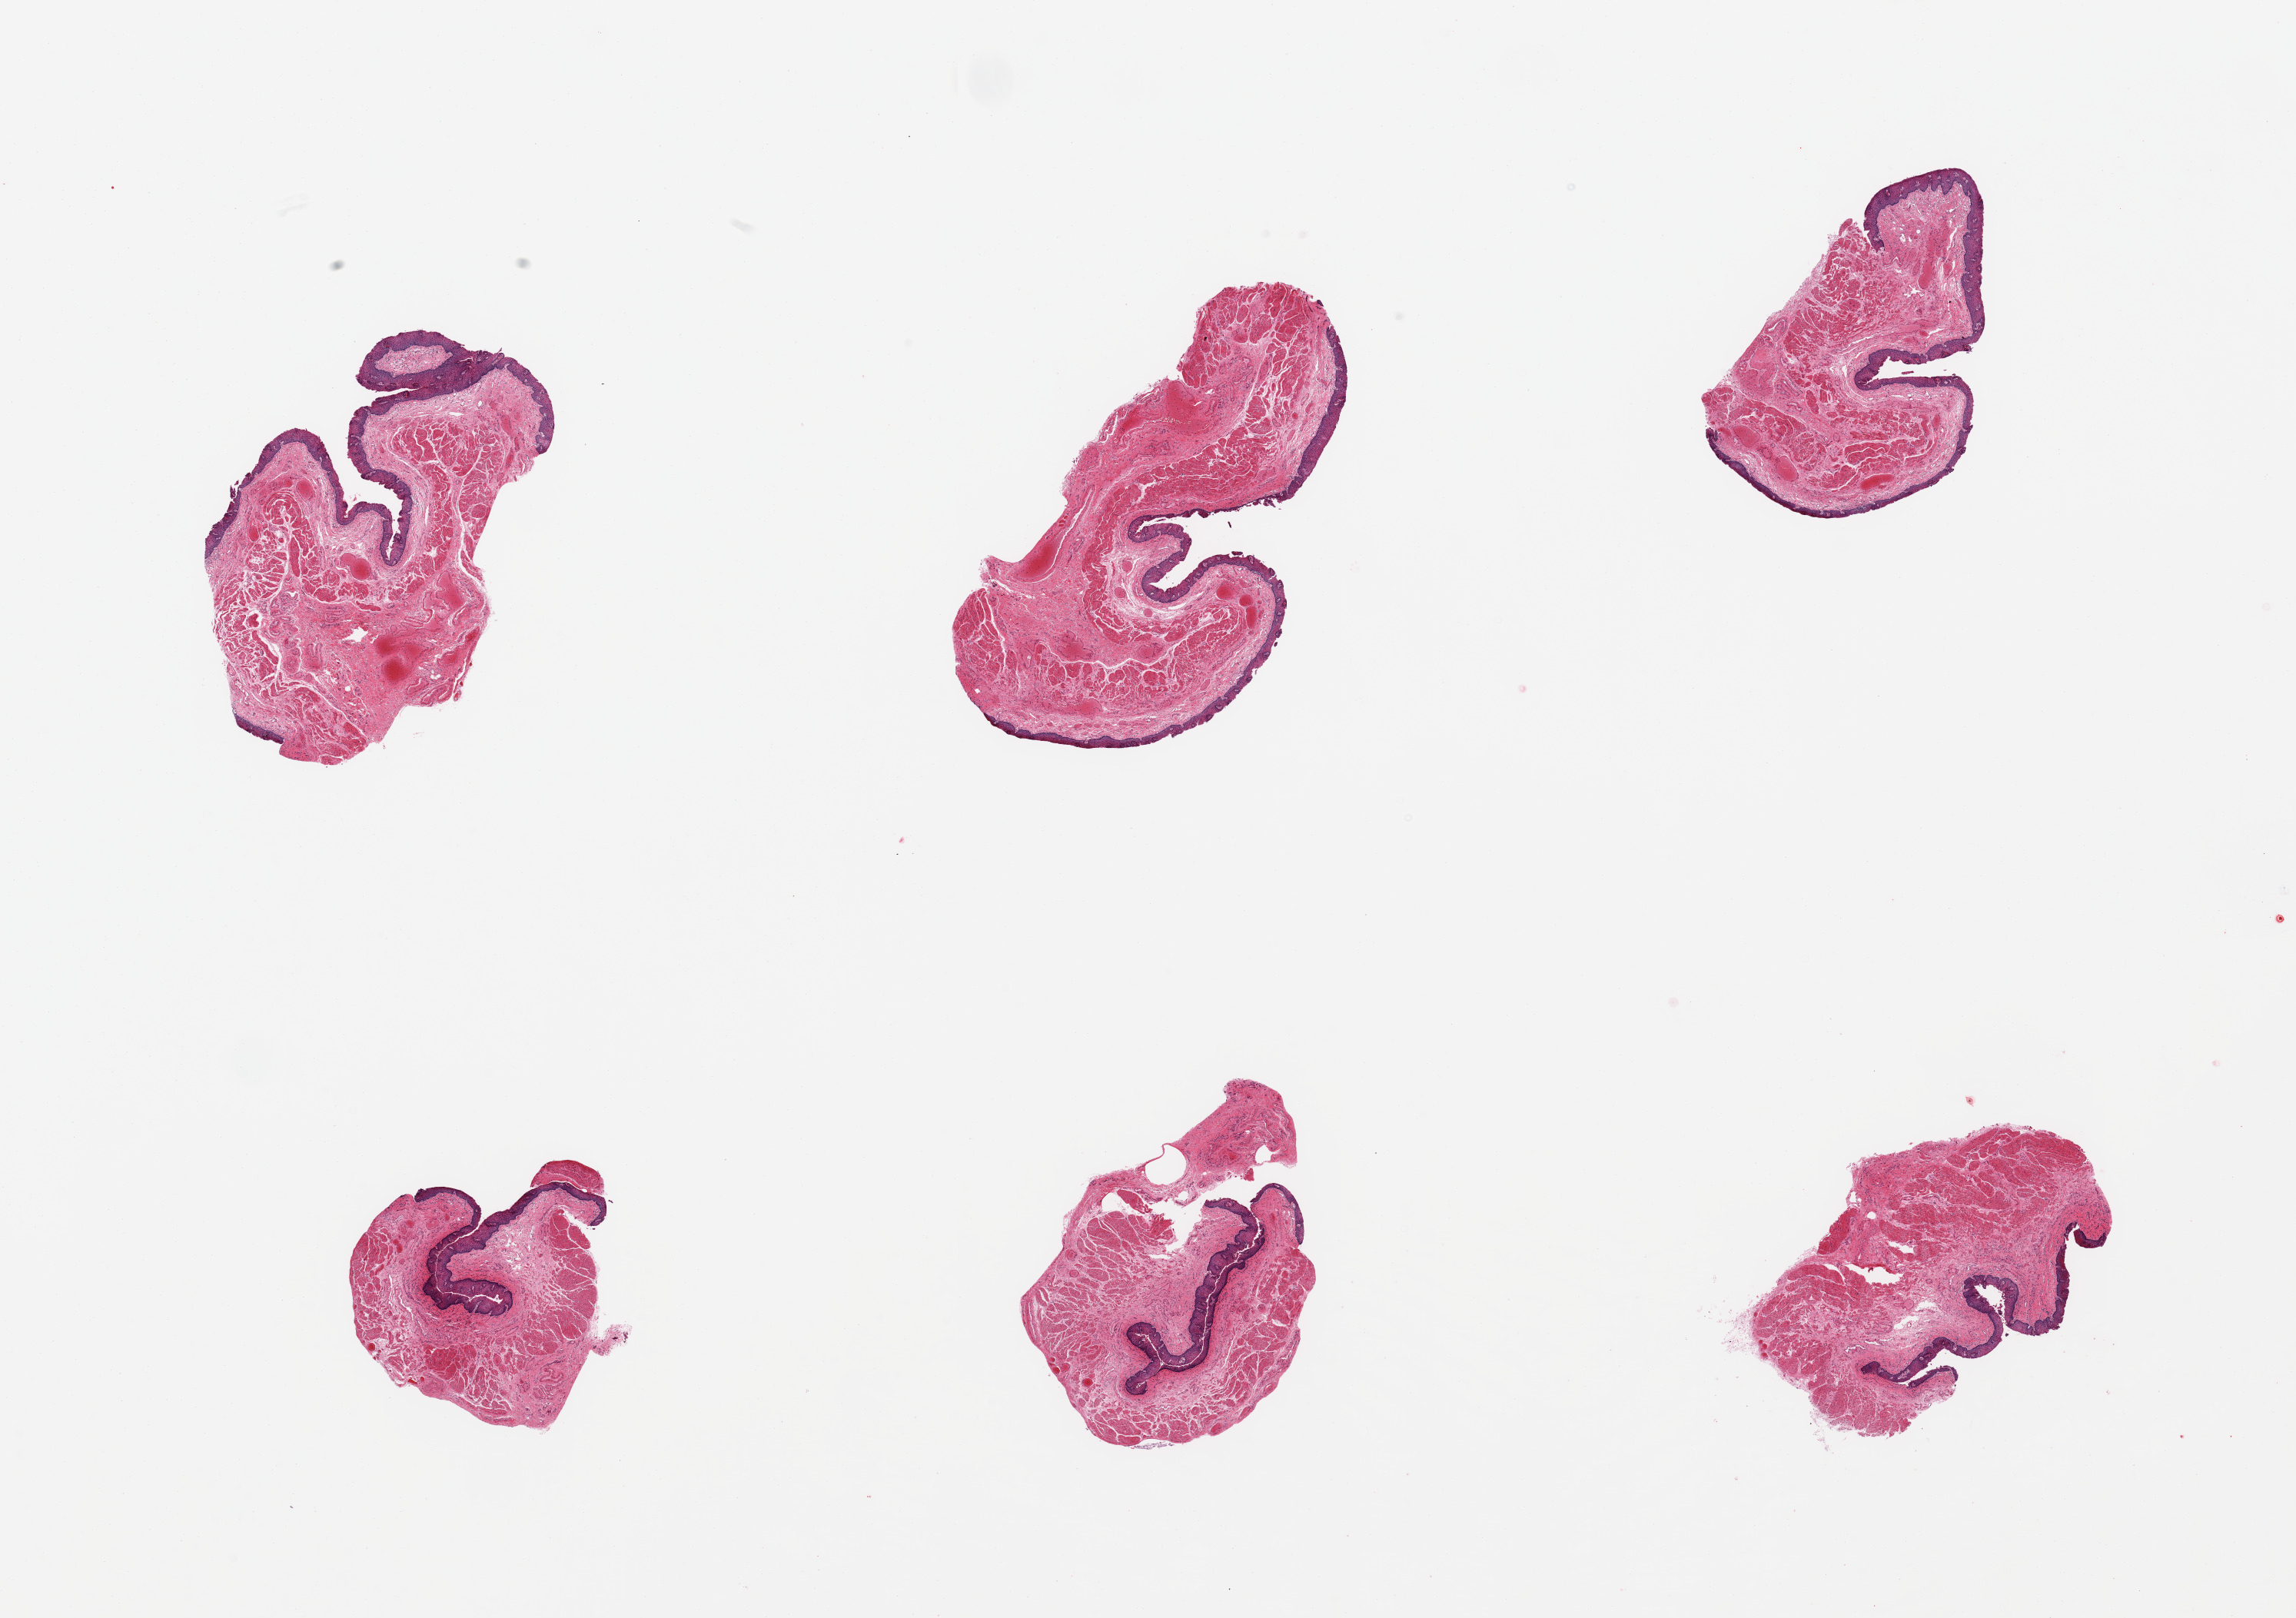
Digitized H&E-stained section, brightfield, a low-resolution overview of the entire scanned area, about 23.6 x 16.6 mm. PAXgene-fixed paraffin-embedded (PFPE) section. Target tissue: esophageal mucous membrane. Tissue donor sample. Donor: male.
* reviewer comment on this tissue sample: 6 pieces; focal sloughing of epithelium; prominent muscularis mucosae